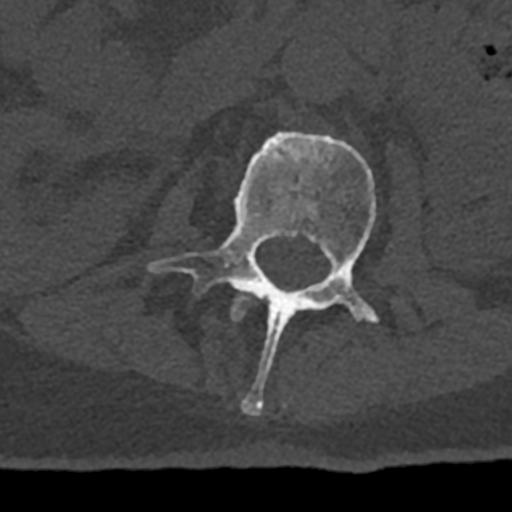
CT including the spine, one axial slice. Slice 380 of 797 in the series (ordered by position). Bone window (W 1800 / L 400 HU). 0.5 mm slice thickness. 512 × 512 image matrix, field of view 160 × 160 mm. Male patient, age 74 years. Case-level facts recorded for this patient, not image findings: primary cancer: renal; vertebrae with lytic lesions (as recorded): T10, L1, L2, L3, L4, L5.
Outlined on this slice (semi-automatically segmented with operator editing):
- L1 vertebra: box from (x=231, y=291) to (x=249, y=322) px
- L2 vertebra: (x=147, y=131)–(x=380, y=416)